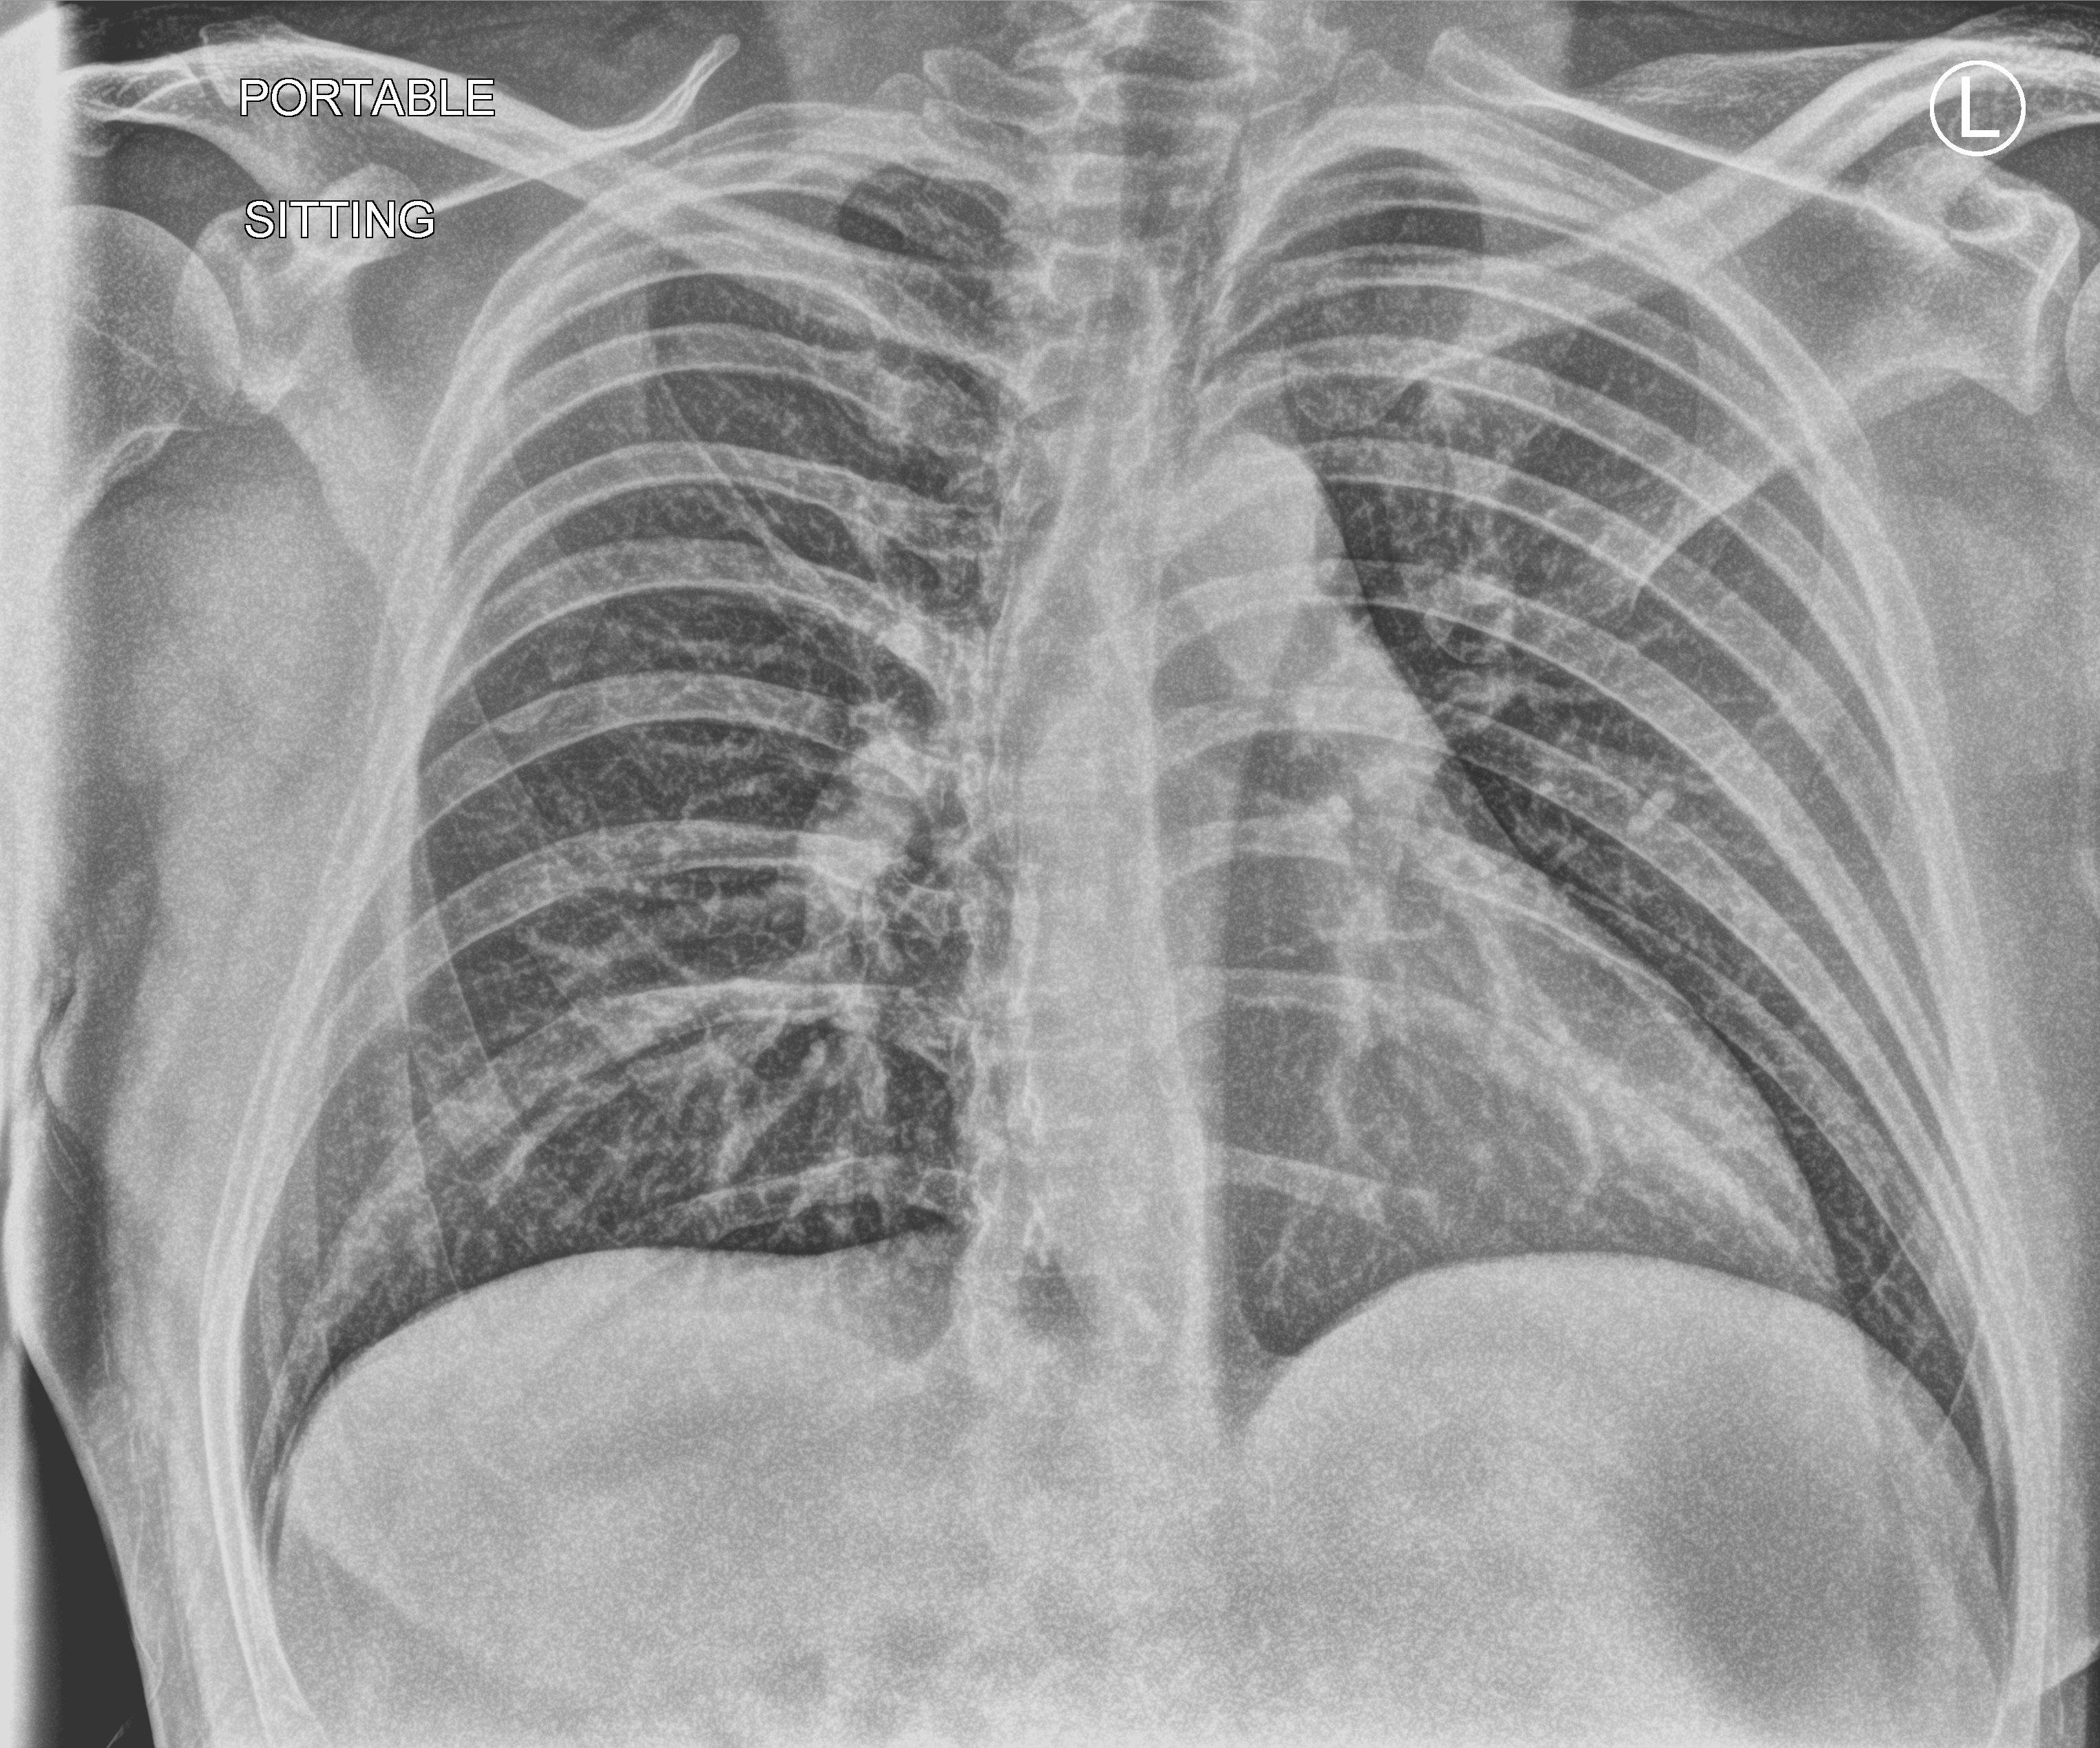
Chest X-ray (portable), anteroposterior (AP) projection. Male patient hospitalised with COVID-19, age 18–59 years.
Admission-level facts for this patient (not findings on this image; timing relative to this image not recorded):
- mechanically ventilated during this hospital stay: no
- COPD (admission record): no
- smoking status (admission record): never